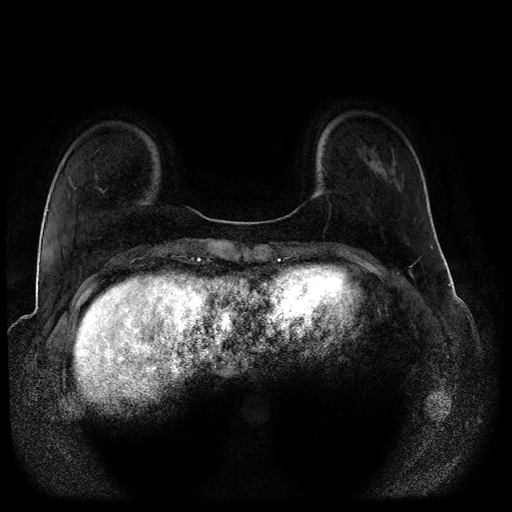
Breast MRI (dynamic contrast-enhanced, multi-phase), one axial slice. Position 27 of 116 along the scan axis. Dynamic contrast-enhanced series, time point 2 of 5 at this slice position (early post-contrast). 1.5 T. TE 2.6 ms, TR 5.3 ms. 2 mm slice thickness. 512 × 512 image matrix. Female patient, age 44 years.
Outlined on this slice (semi-automatically segmented with operator editing):
- breast lesion (labelled benign in the annotation): box from (x=371, y=161) to (x=384, y=173) px